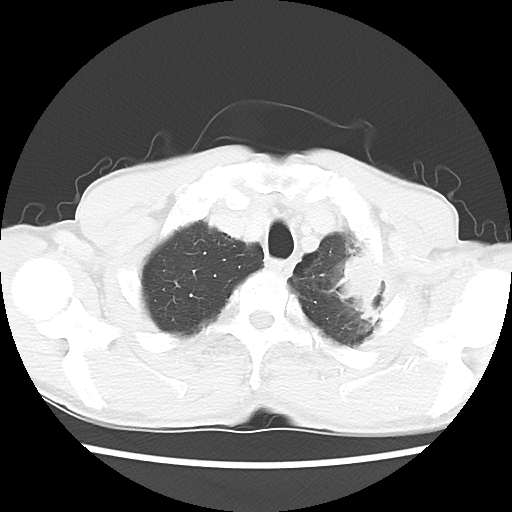
Chest CT, one axial slice; slice 53 of 60 in the series (ordered by position); reconstruction kernel LUNG; 120 kVp; lung window (W 1500 / L -600 HU); 512 × 512 image matrix, field of view 308 × 308 mm. Male patient, age 64 years. Case-level facts recorded for this patient, not image findings: clinical TNM (as recorded): T3 N3 M0; histopathological grade: G3.
Annotated regions visible in this slice (bounding box drawn by a radiologist):
- lung tumour (recorded histology: adenocarcinoma): bounding box [x1, y1, x2, y2] px = [334, 245, 391, 321]